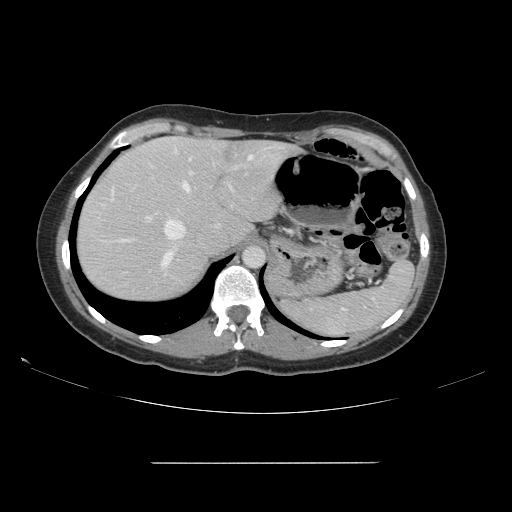
Contrast-enhanced abdominal CT, one axial slice. Slice 118 of 151 in the series (ordered by position). 120 kVp. Intravenous contrast given. Soft-tissue window (W 400 / L 40 HU). 2.5 mm slice thickness. 512 × 512 image matrix, field of view 421 × 421 mm. Female patient, age 46 years. From the clinical record (not read from this slice): diagnosis: colorectal cancer liver metastases, imaged before liver resection; multiple liver metastases: yes; largest metastasis: 3 cm; disease in both lobes: yes.
Annotated regions visible in this slice (outlined manually by an expert reader):
- hepatic veins: bounding box [x1, y1, x2, y2] px = [112, 154, 255, 241]
- liver: [77, 137, 298, 303]
- planned liver remnant (the part of the liver to remain after resection): [90, 137, 294, 250]
- portal vein (with intrahepatic branches): [162, 168, 235, 268]
- liver metastasis: [223, 147, 235, 163]